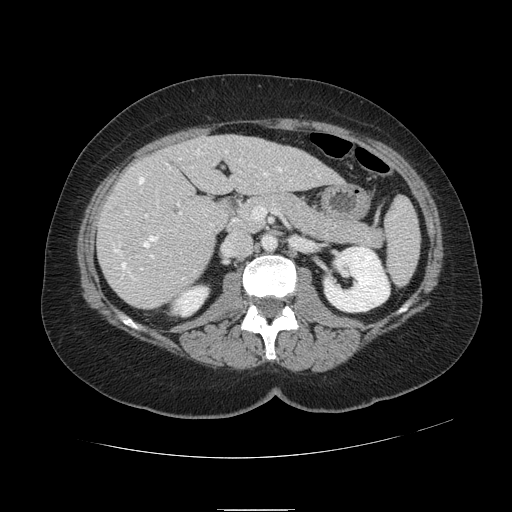
Contrast-enhanced abdominal CT, one axial slice; 120 kVp; intravenous contrast given; soft-tissue window (W 400 / L 40 HU); 2.5 mm slice thickness; 512 × 512 image matrix, field of view 400 × 400 mm. Female patient, age 52 years. From the clinical record (not read from this slice): diagnosis: colorectal cancer liver metastases, imaged before liver resection; multiple liver metastases: yes; largest metastasis: 6.3 cm; chemotherapy before resection: yes.
Outlined on this slice (expert manual segmentation):
- hepatic veins: box from (x=114, y=150) to (x=282, y=277) px
- liver: (x=99, y=135)–(x=340, y=308)
- planned liver remnant (the part of the liver to remain after resection): (x=176, y=135)–(x=340, y=195)
- portal vein (with intrahepatic branches): (x=125, y=203)–(x=182, y=270)